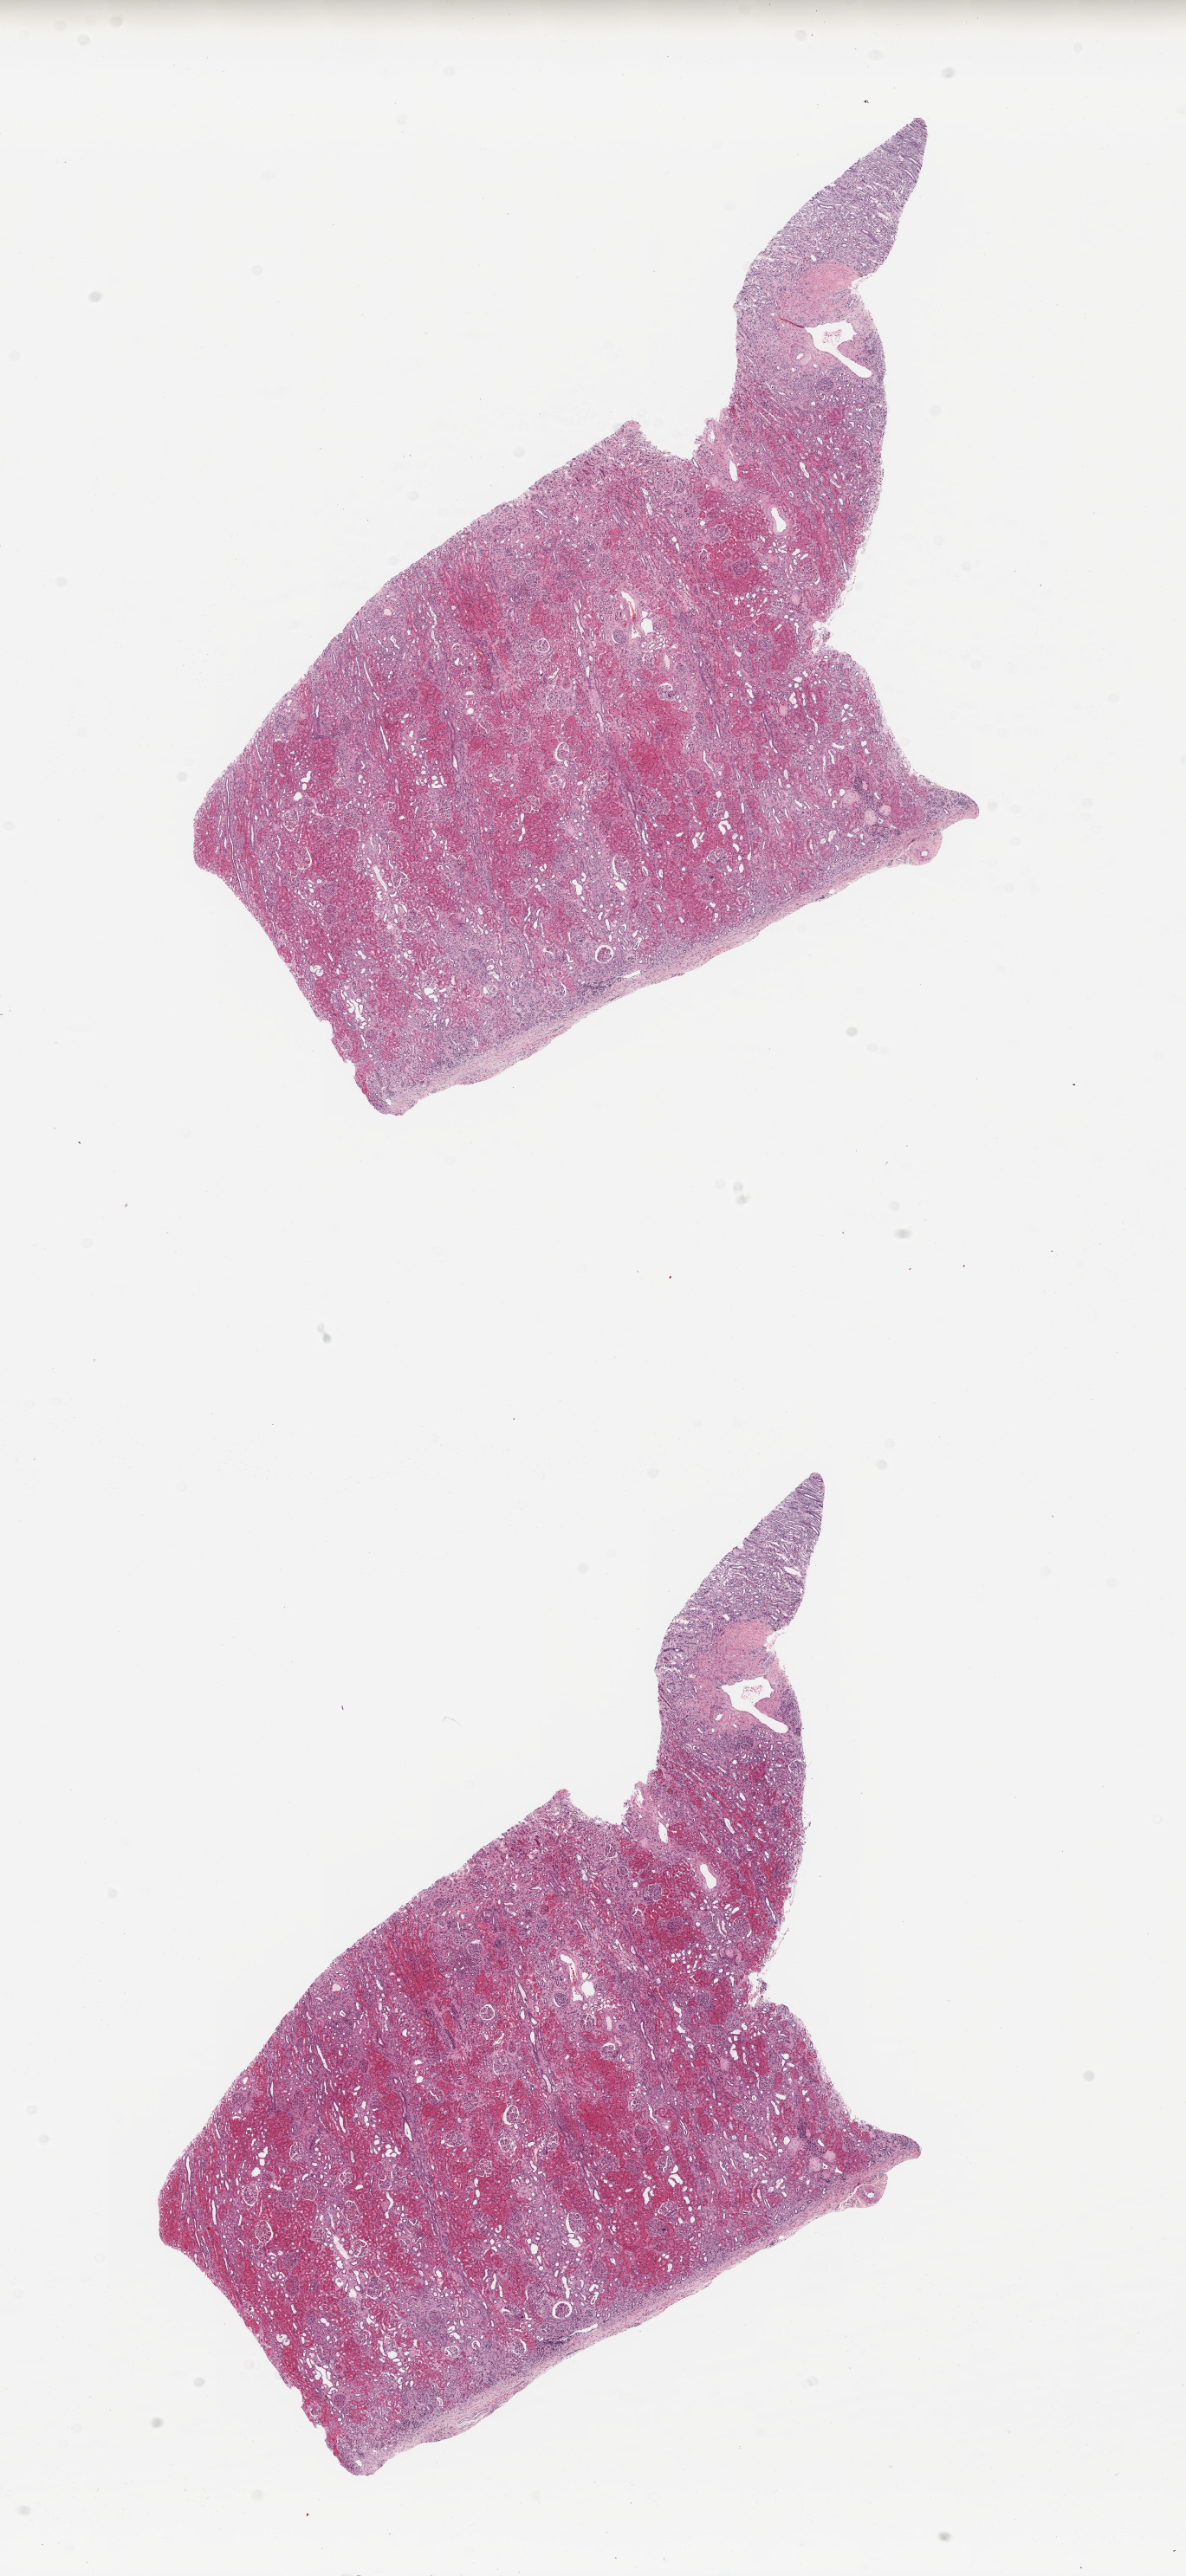
Digitized H&E tissue section (whole slide), a low-resolution overview of the entire scanned area, about 10.8 x 23.5 mm; normal (non-tumour) tissue sample, sampled site: kidney. 56-year-old male patient.
This section: normal (non-tumour) tissue from the same patient. Patient diagnosis: Renal cell carcinoma, NOS.